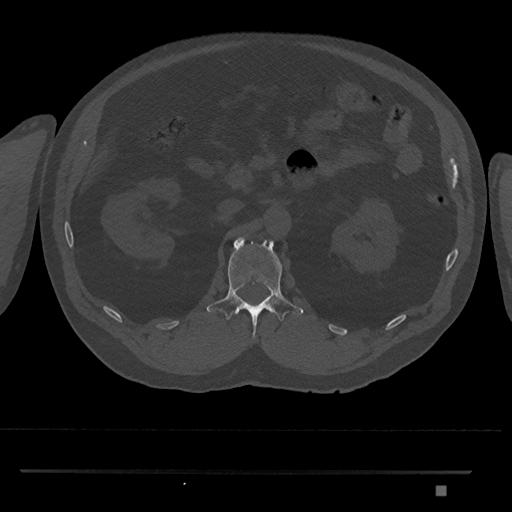
CT including the spine, one axial slice. Reconstruction kernel Br40s/3. Bone window (W 1800 / L 400 HU). 0.5 mm slice thickness. 512 × 512 image matrix, field of view 429 × 429 mm. Patient: male, 65 years. From the clinical record (not read from this slice): primary cancer: prostate.
Annotated regions visible in this slice (semi-automatically segmented with operator editing):
- L1 vertebra: bounding box (x1, y1, x2, y2) in pixels: (207, 237, 303, 338)